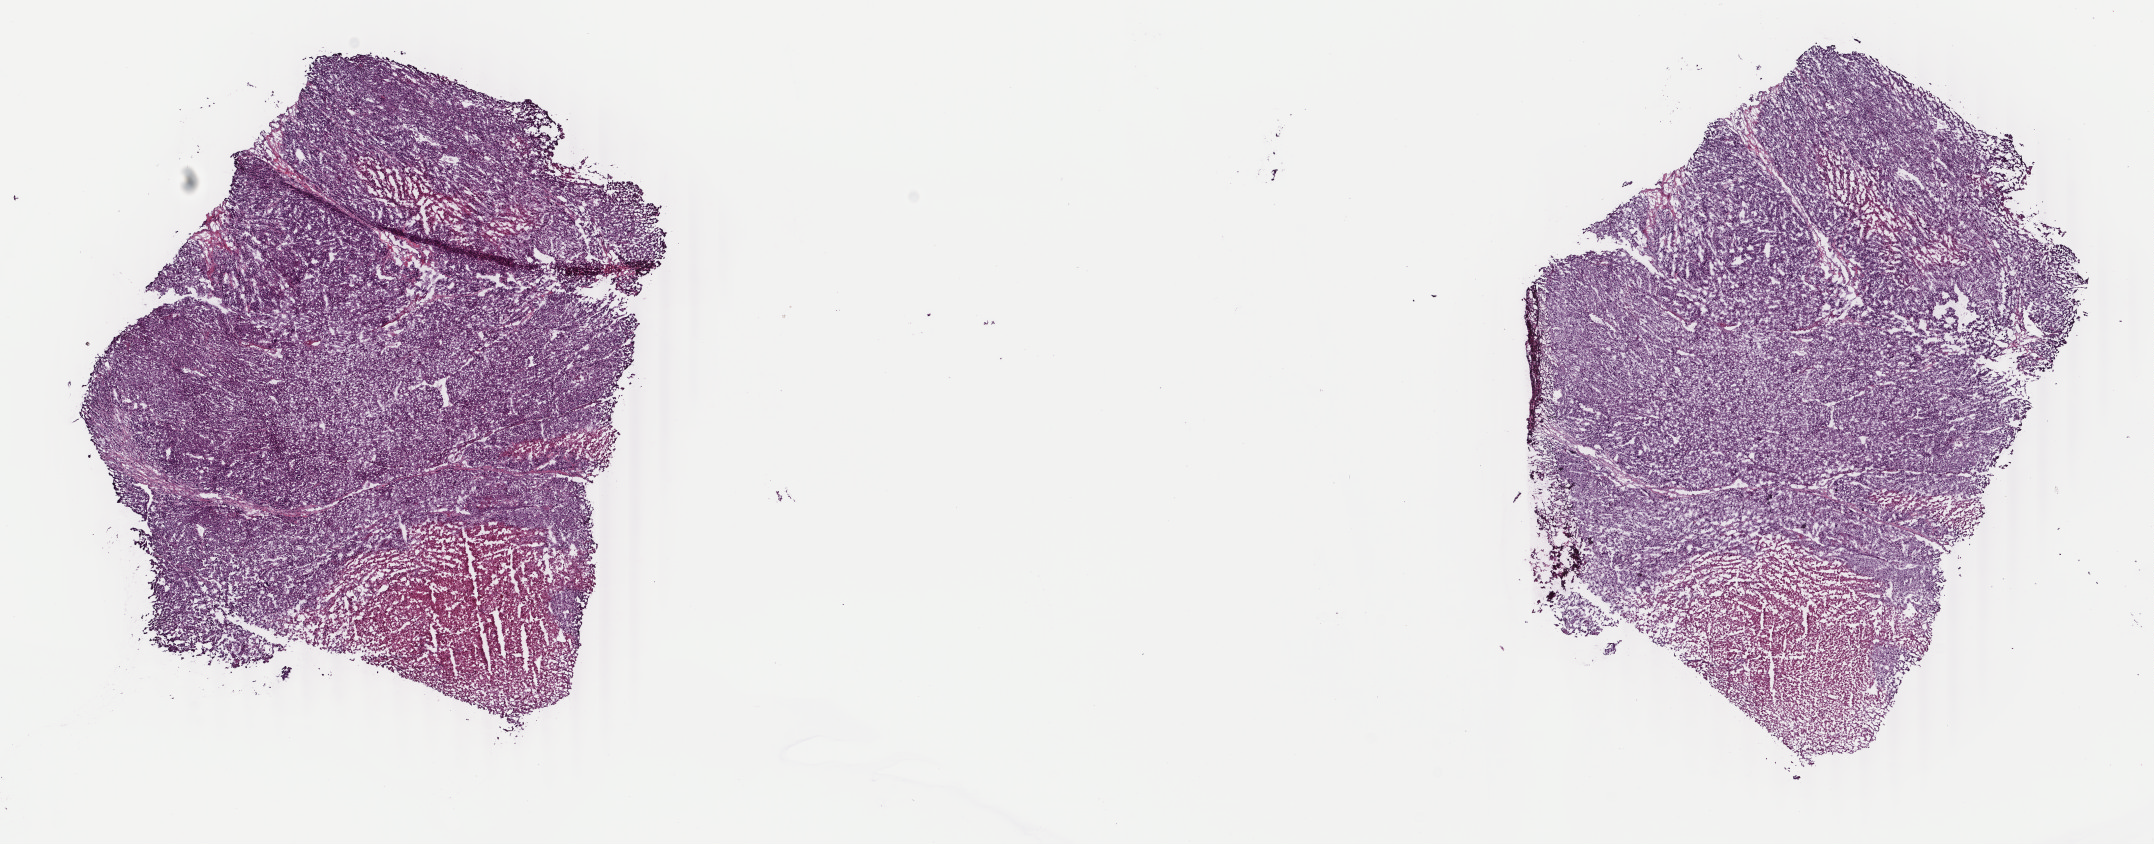
Whole-slide histology image, H&E — shown as a low-resolution overview of the whole scanned area (about 17.1 x 6.7 mm). Frozen section. Primary tumour sample from the adrenal cortex. Patient: female, age at initial diagnosis 23 years. Pathologist review of this section (percent, as recorded): tumour cells 82%, tumour nuclei 80%, normal cells 0%, stromal cells 0%, necrosis 18%. Infiltration values recorded for this section: lymphocyte infiltration 2%, monocyte infiltration 0%, neutrophil infiltration 0%.
Lymph nodes positive (case pathology): 2 of 2 examined. Diagnosis: Adrenal cortical carcinoma (cortex of adrenal gland).